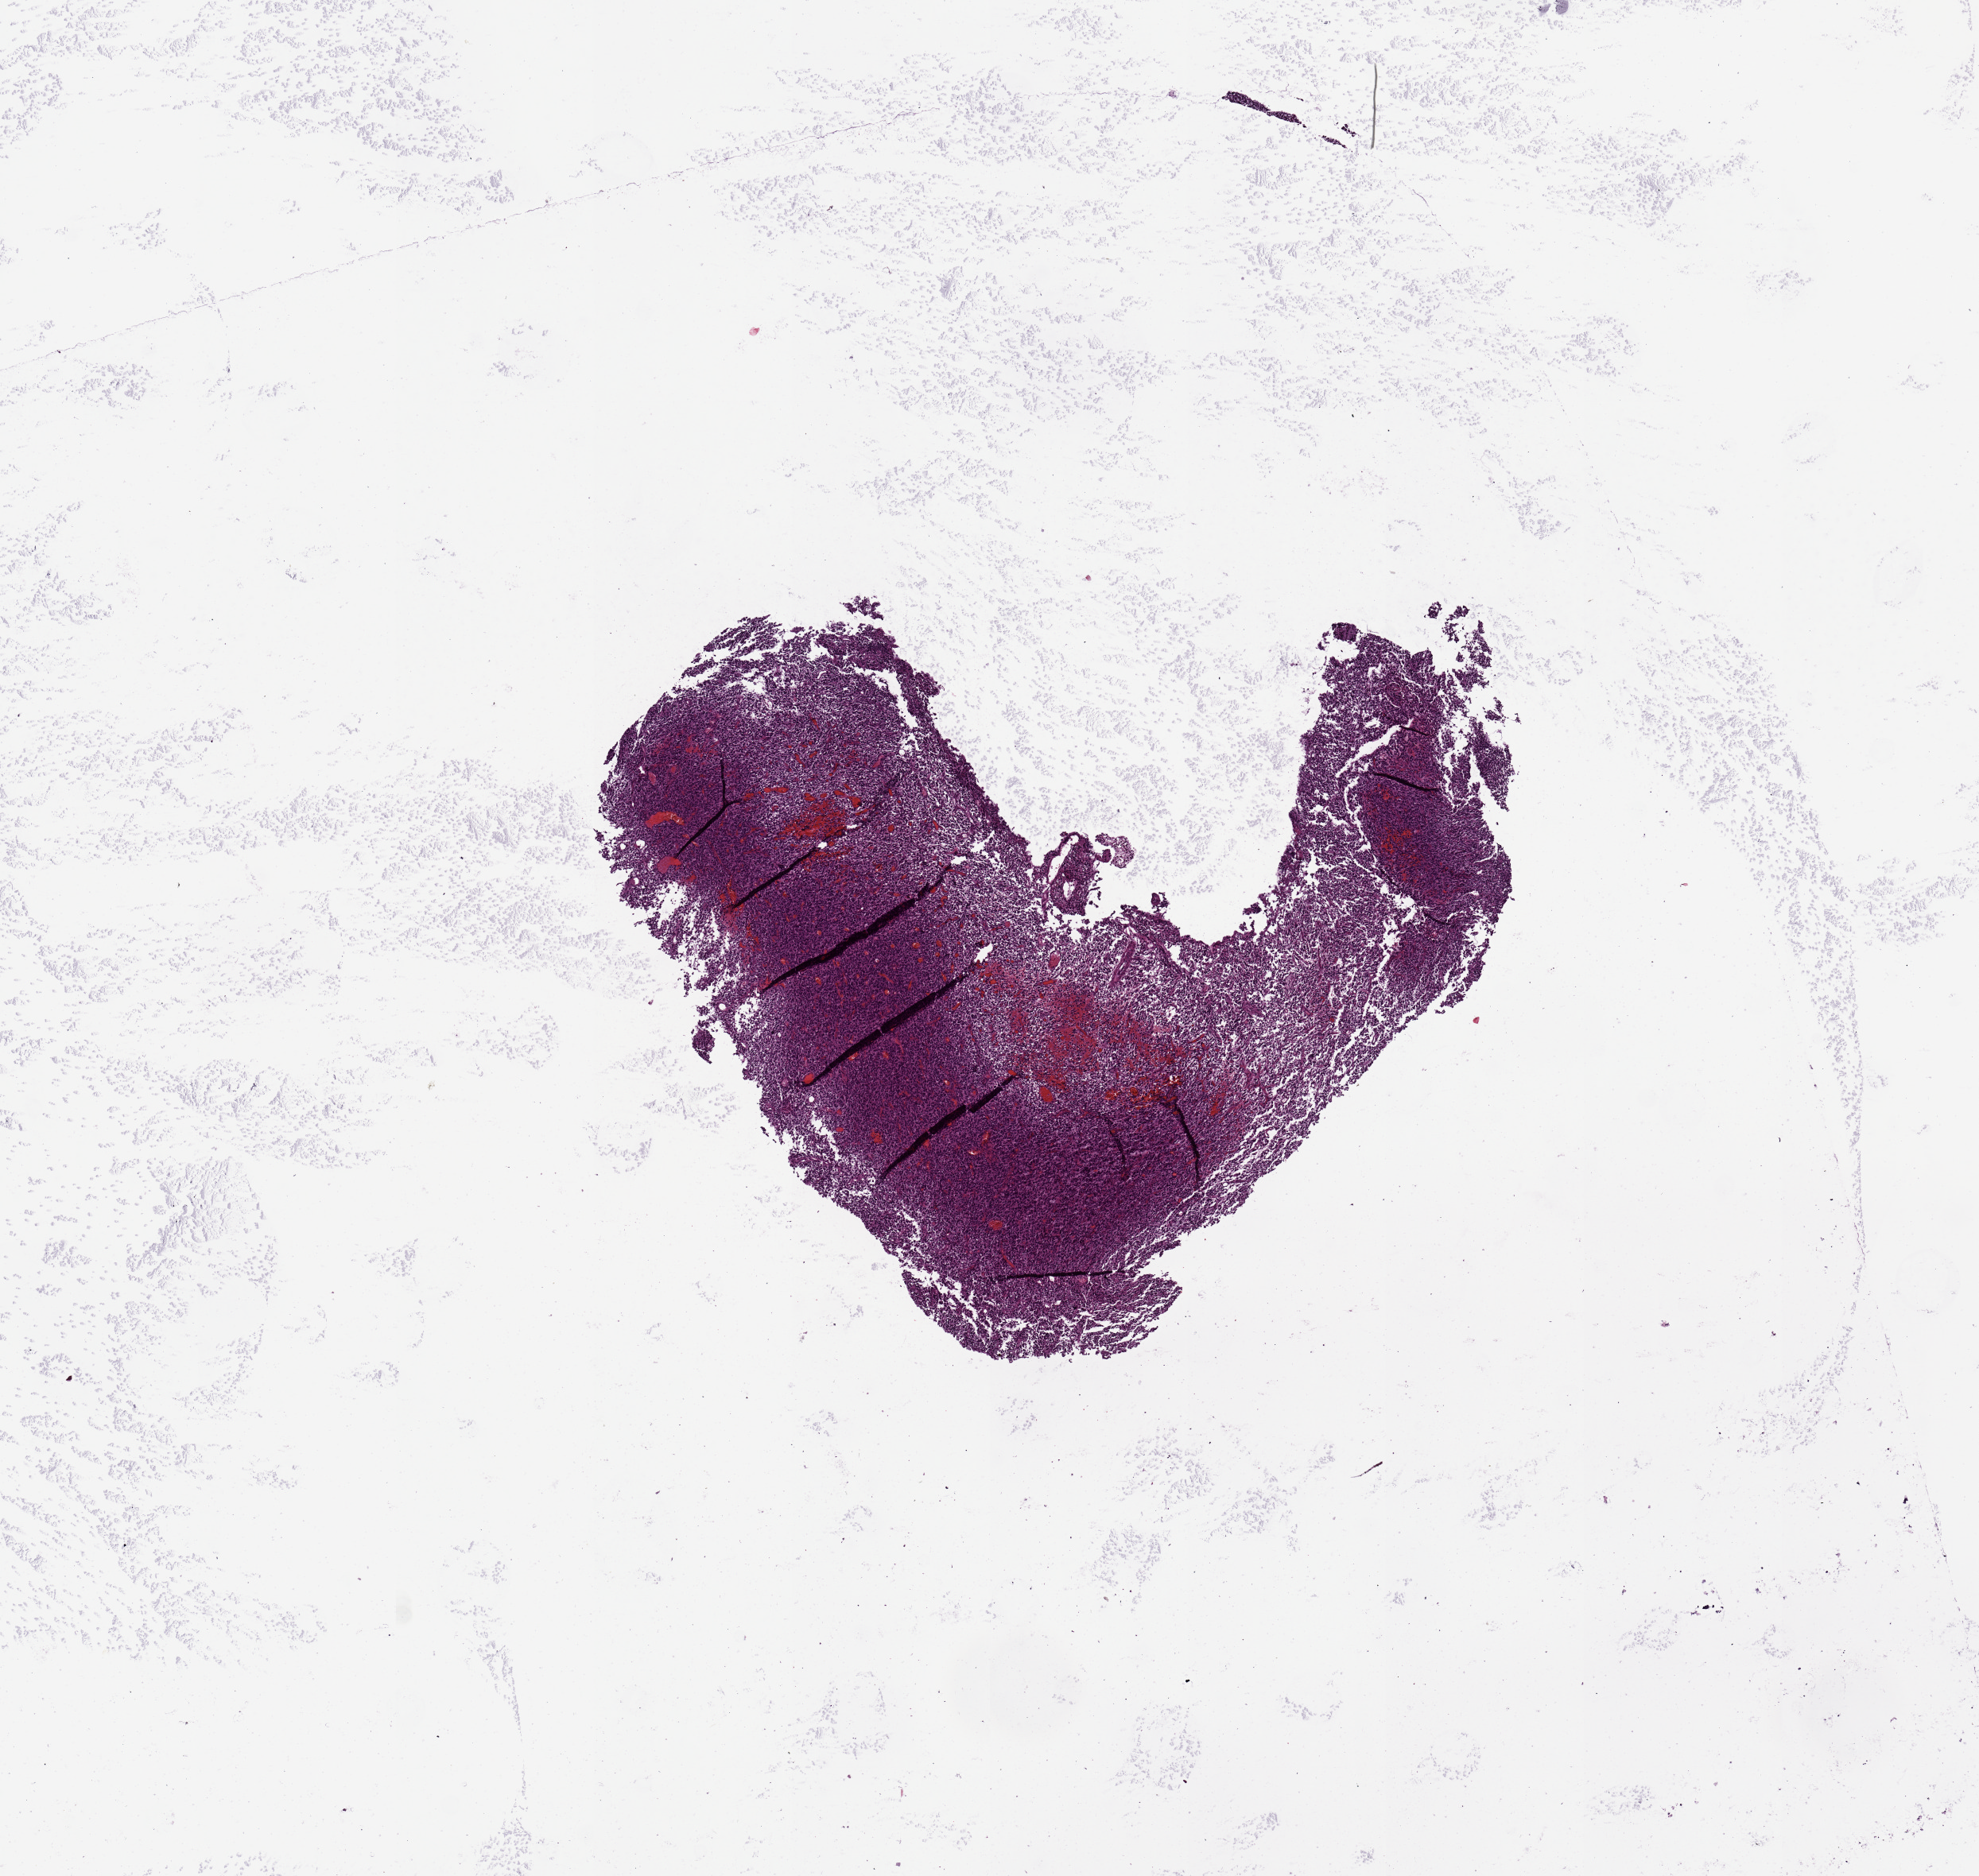
Digitized H&E tissue section (whole slide) — low-resolution overview of the scanned area, about 9.8 x 9.3 mm (acquisition: 20x scan); tumour tissue sample, sampled site: brain. Male, 35 y/o. Pathologist review of this section (percent, as recorded): tumour nuclei 80%, necrosis 5%.
* diagnosis: Glioblastoma